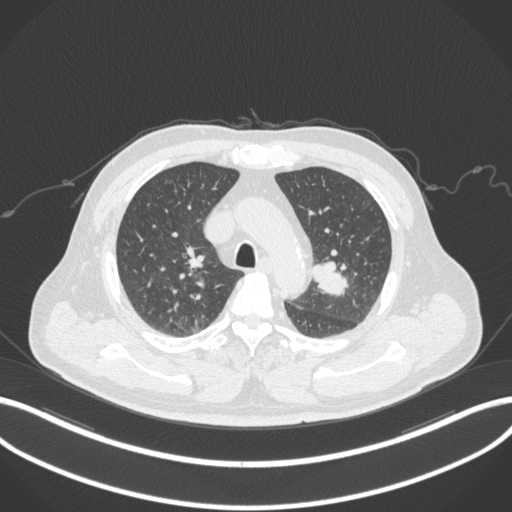
Chest CT, one axial slice. Reconstruction kernel B31f. 120 kVp. Lung window (W 1500 / L -600 HU). 1 mm slice thickness. 512 × 512 image matrix, field of view 400 × 400 mm. Male patient, age 67 years. Case-level facts recorded for this patient, not image findings: clinical TNM (as recorded): T2a N1 M0.
Annotated regions visible in this slice (rectangle marked by the reading radiologist):
- lung tumour (recorded histology: adenocarcinoma): bounding box (x1, y1, x2, y2) in pixels: (310, 257, 352, 295)